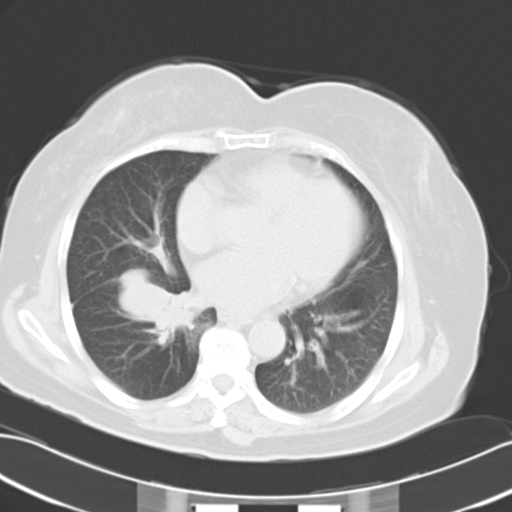
Chest CT, one axial slice; position 12 of 24 along the scan axis; reconstruction kernel B40f; 120 kVp; lung window (W 1500 / L -600 HU); 10 mm slice thickness; 512 × 512 image matrix. Patient: female, 63 years. Case-level facts recorded for this patient, not image findings: clinical TNM (as recorded): T3 N0 M0.
Structures marked on this image (rectangle marked by the reading radiologist):
- lung tumour (recorded histology: adenocarcinoma): bounding box <121,269,197,341> (left, top, right, bottom; pixels)